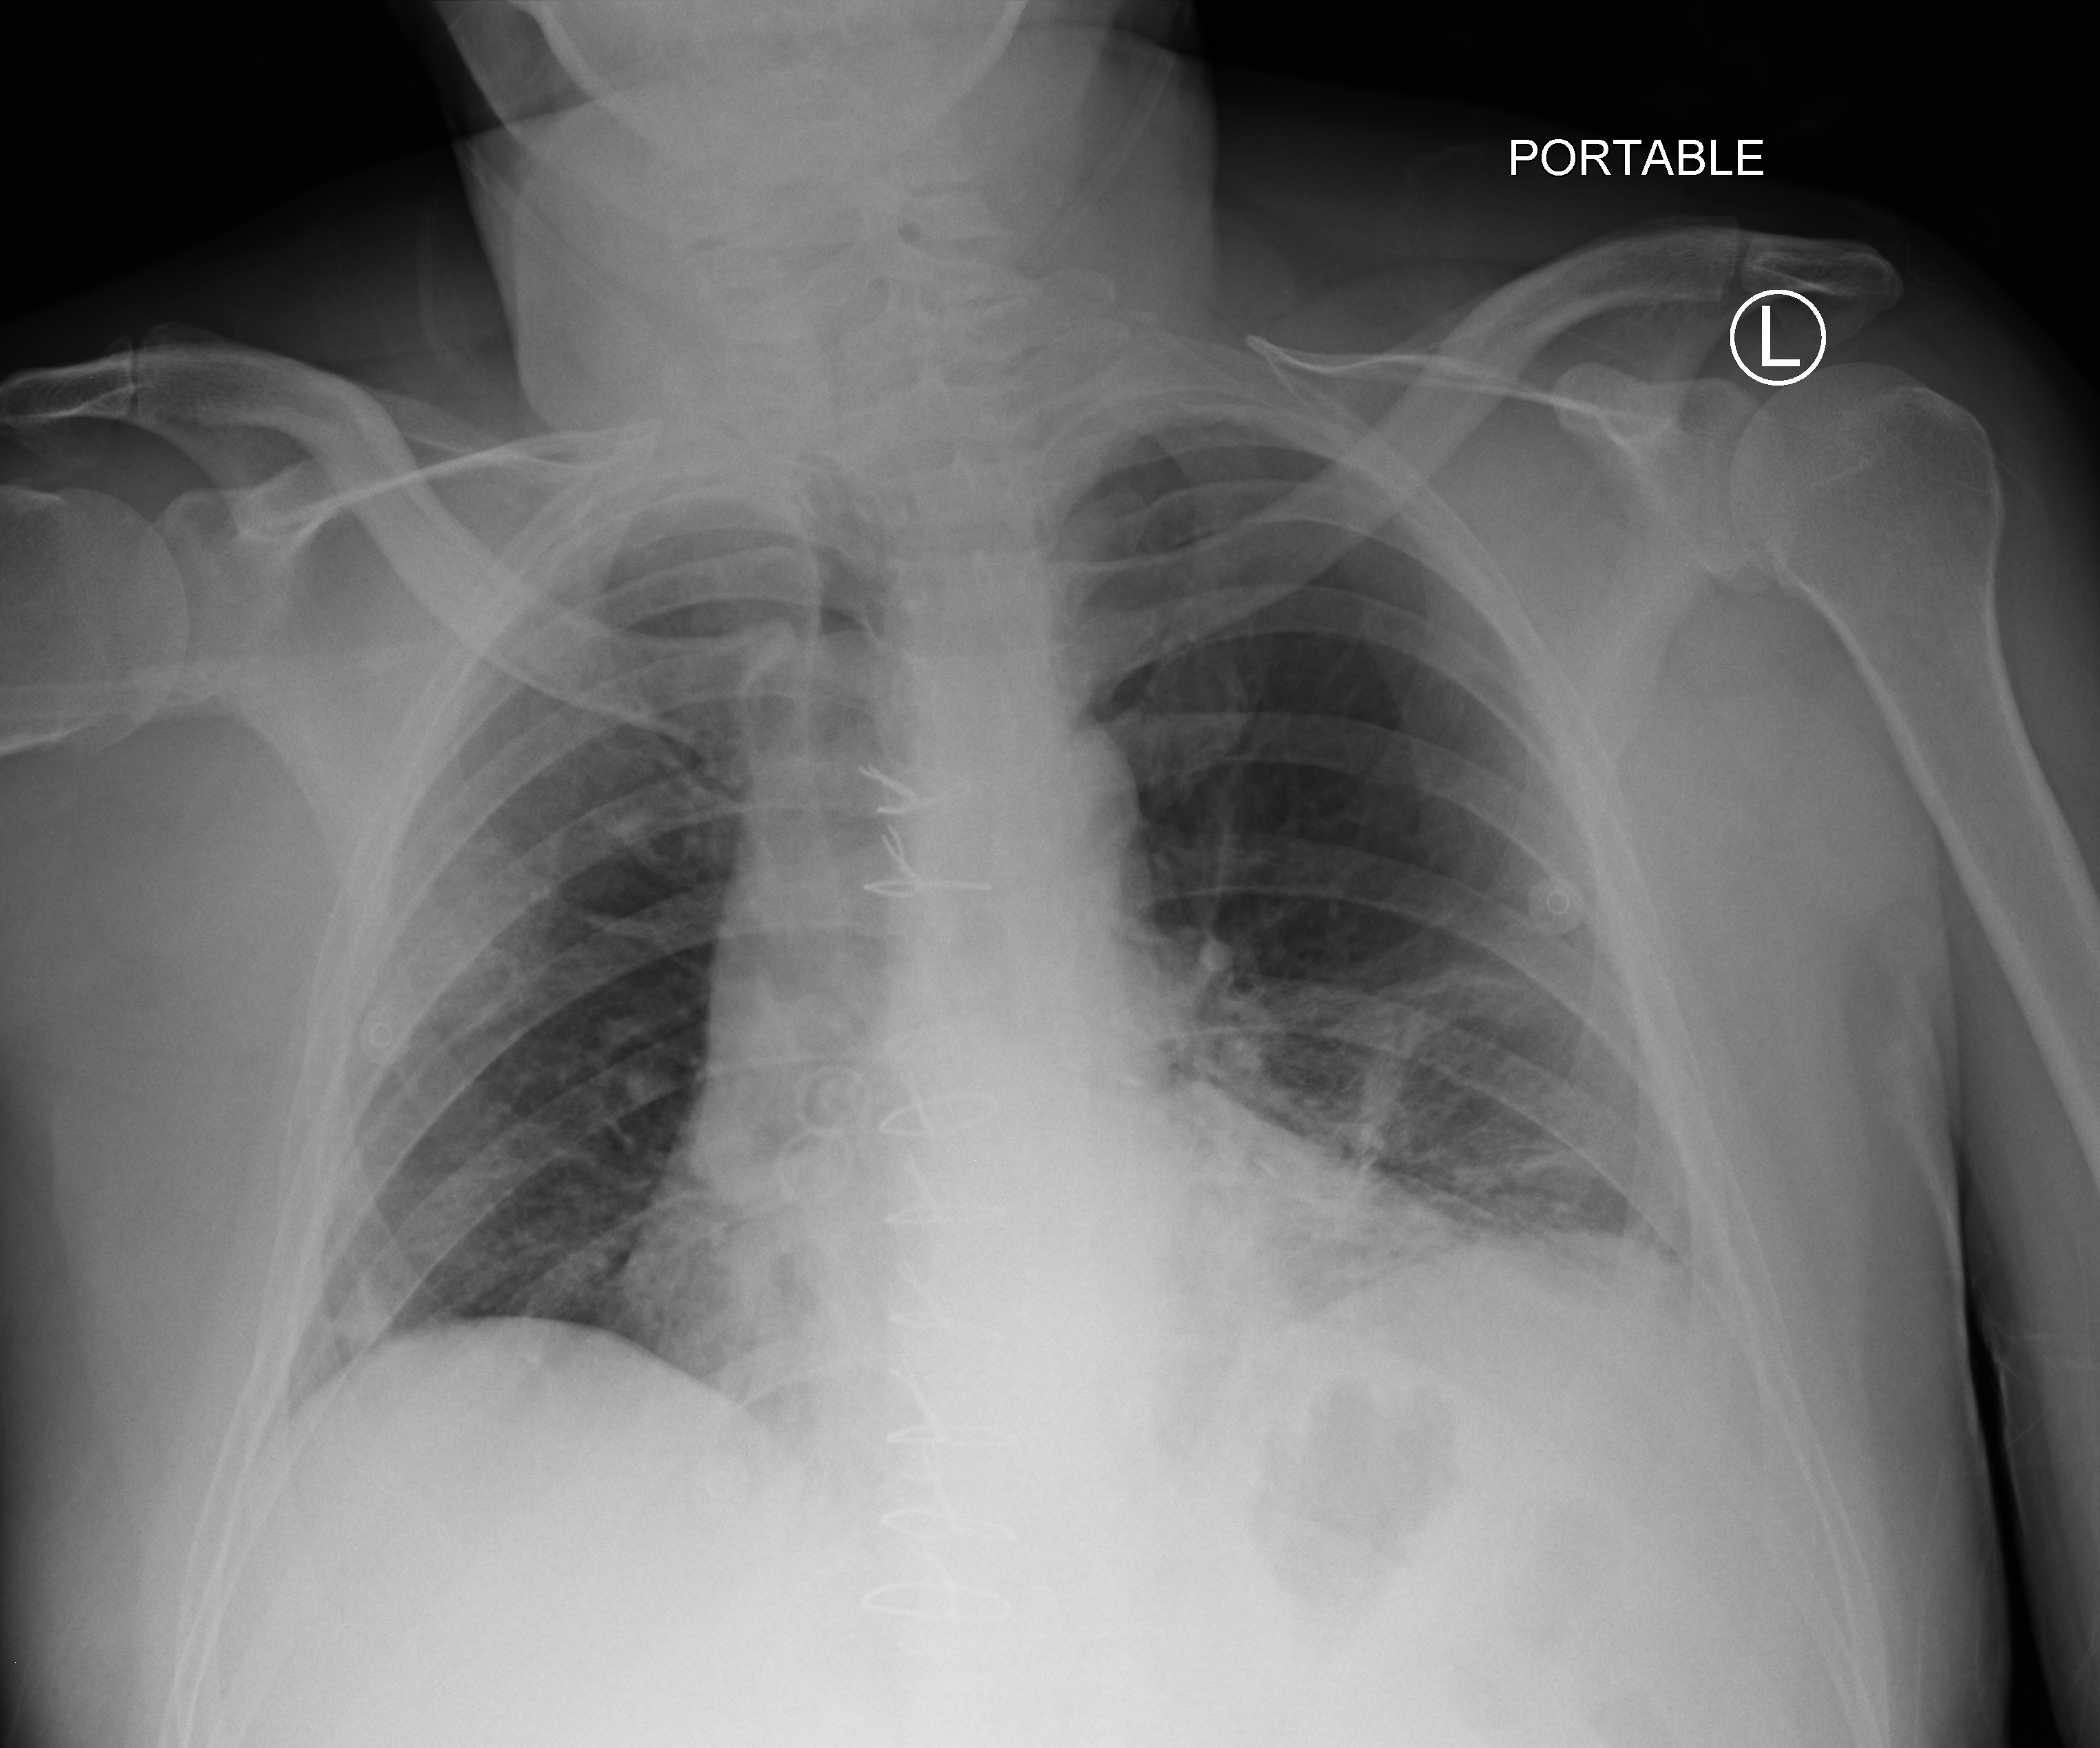
Bedside chest radiograph (computed radiography); anteroposterior (AP) projection. Patient hospitalised with COVID-19; male, aged 18–59 years.
From the hospital-stay record, not from the radiograph (when in the stay this image was taken is not recorded): mechanically ventilated during this hospital stay: yes; length of hospital stay: 63 days; admitted to intensive care during this hospital stay: yes.